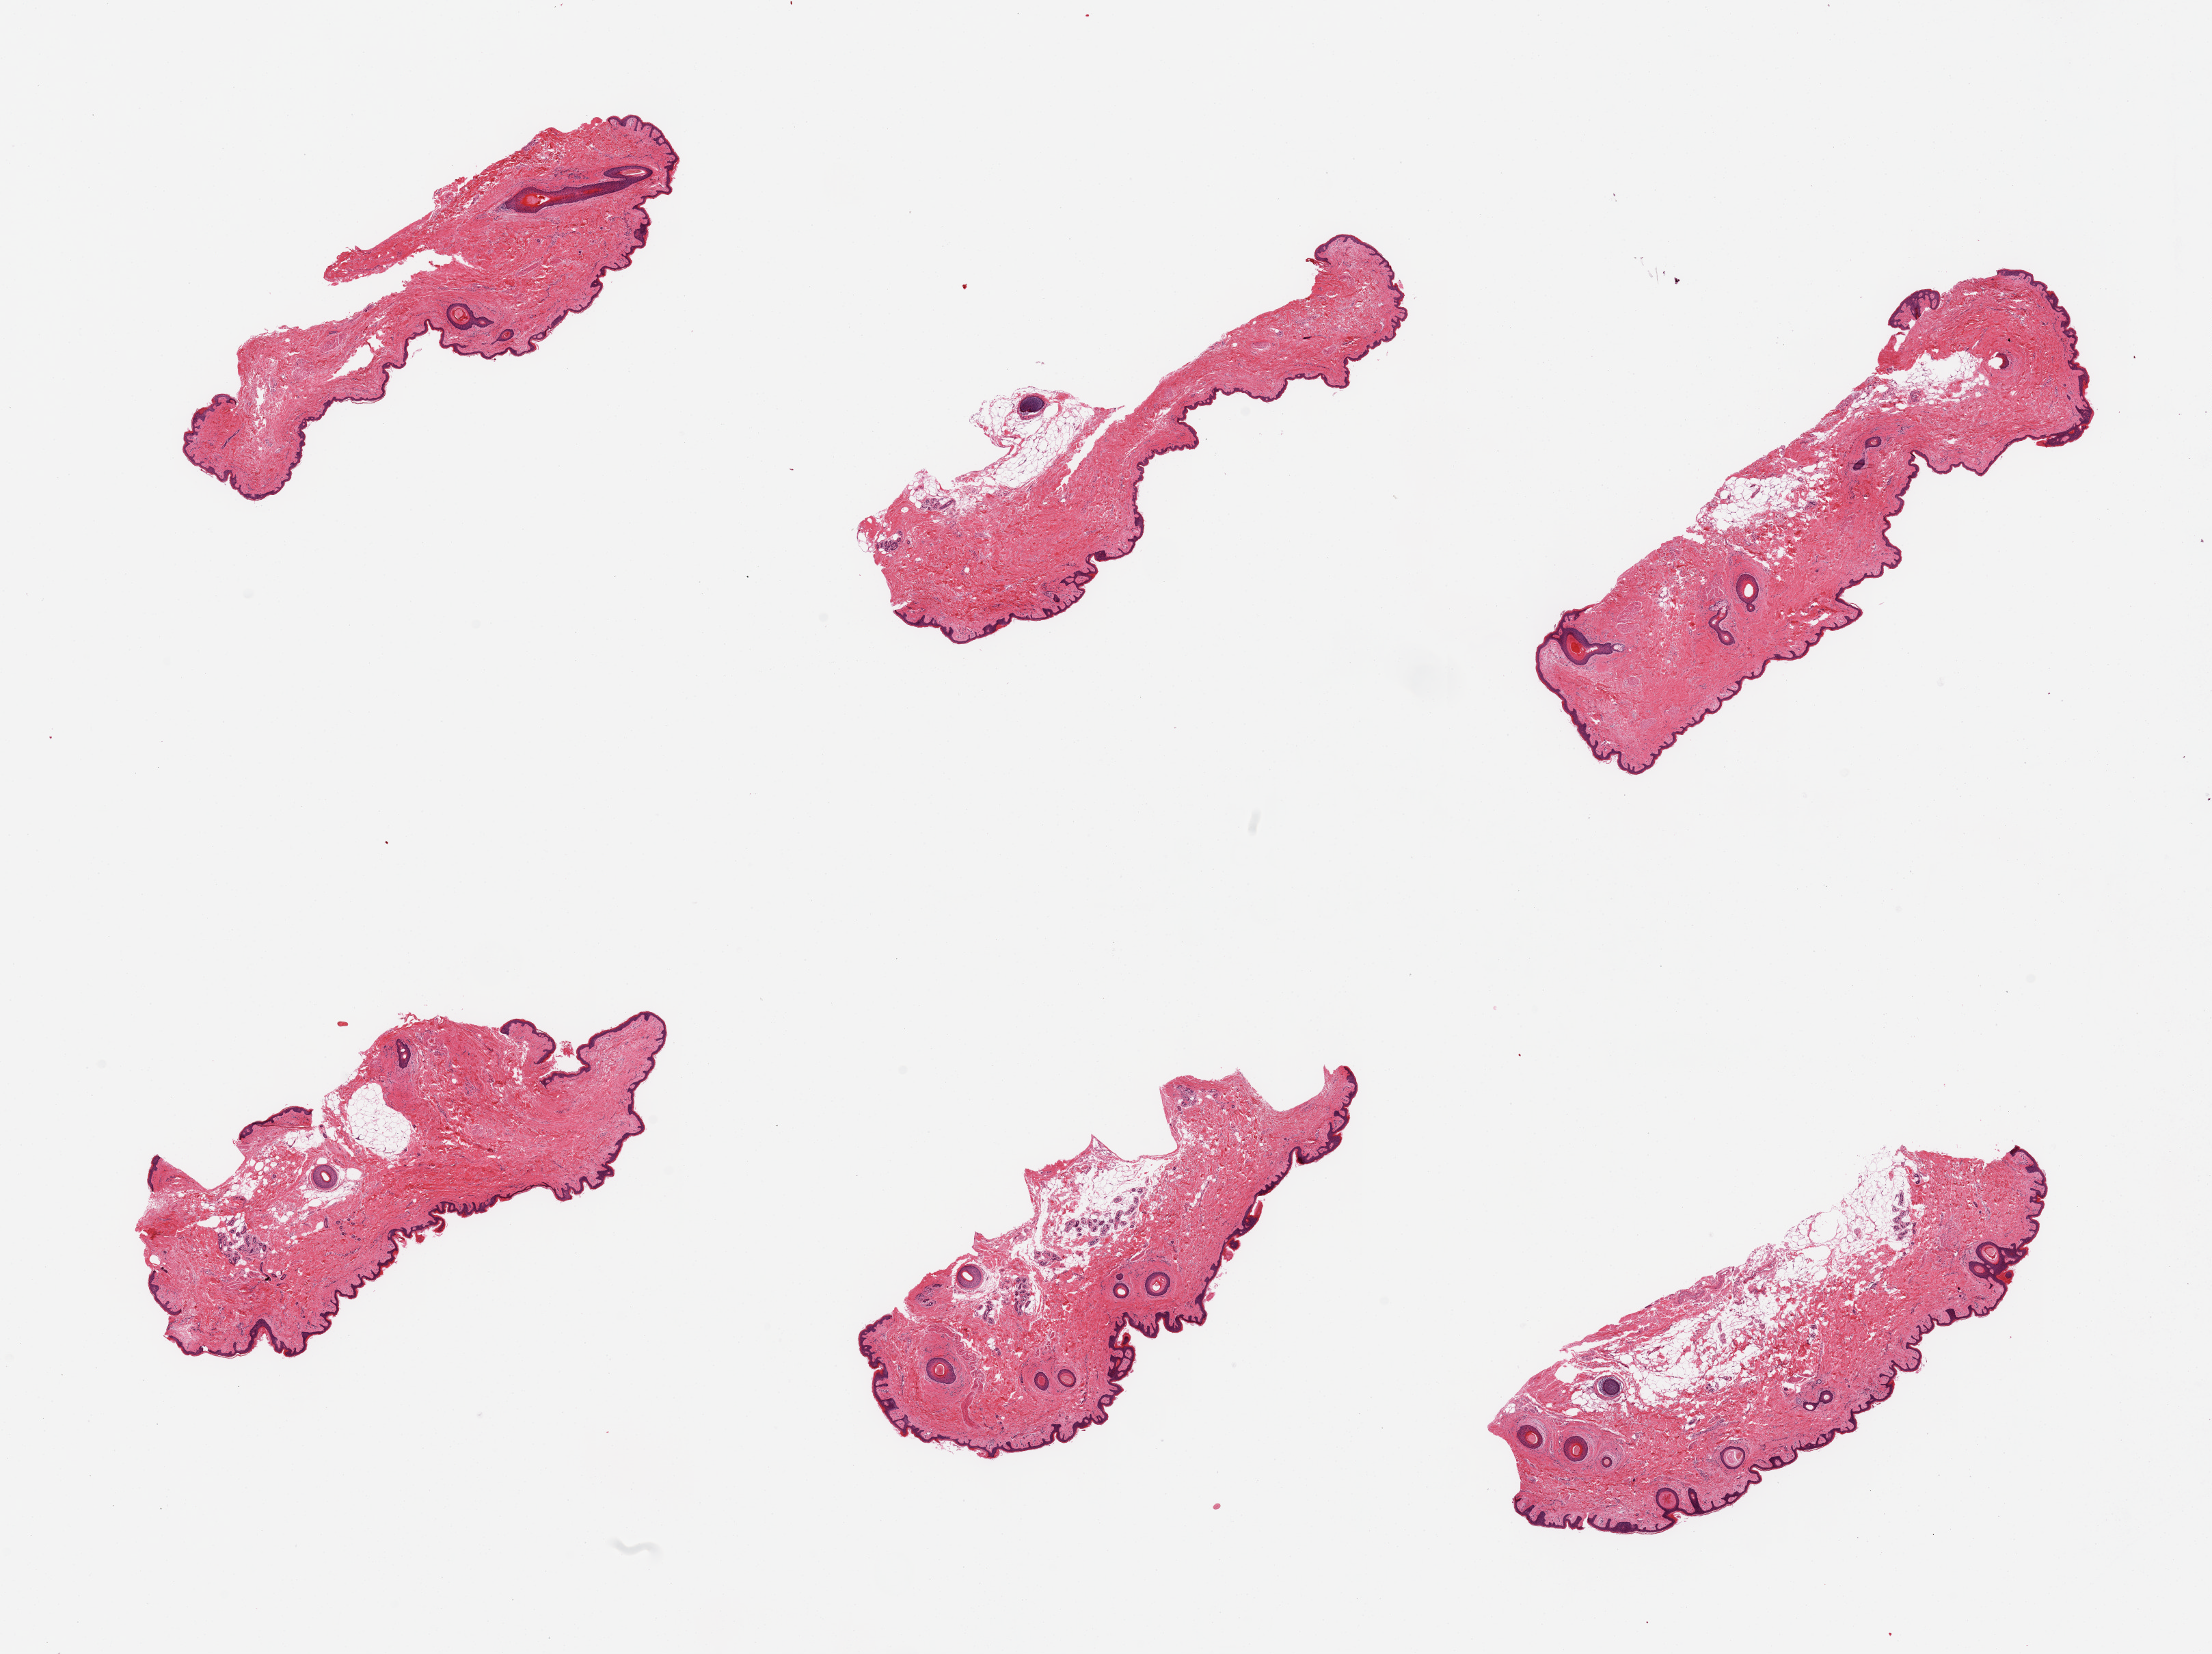
Hematoxylin and eosin (H&E) whole-slide image — shown as a low-resolution overview of the whole scanned area (about 25.6 x 19.1 mm), PAXgene-fixed paraffin-embedded (PFPE) section, section of skin of suprapubic region (target tissue), tissue donor sample. Female donor.
Reviewer comment on this tissue sample: 6 pieces, minimal dermal fat; squamous epithelium is ~50-60microns.